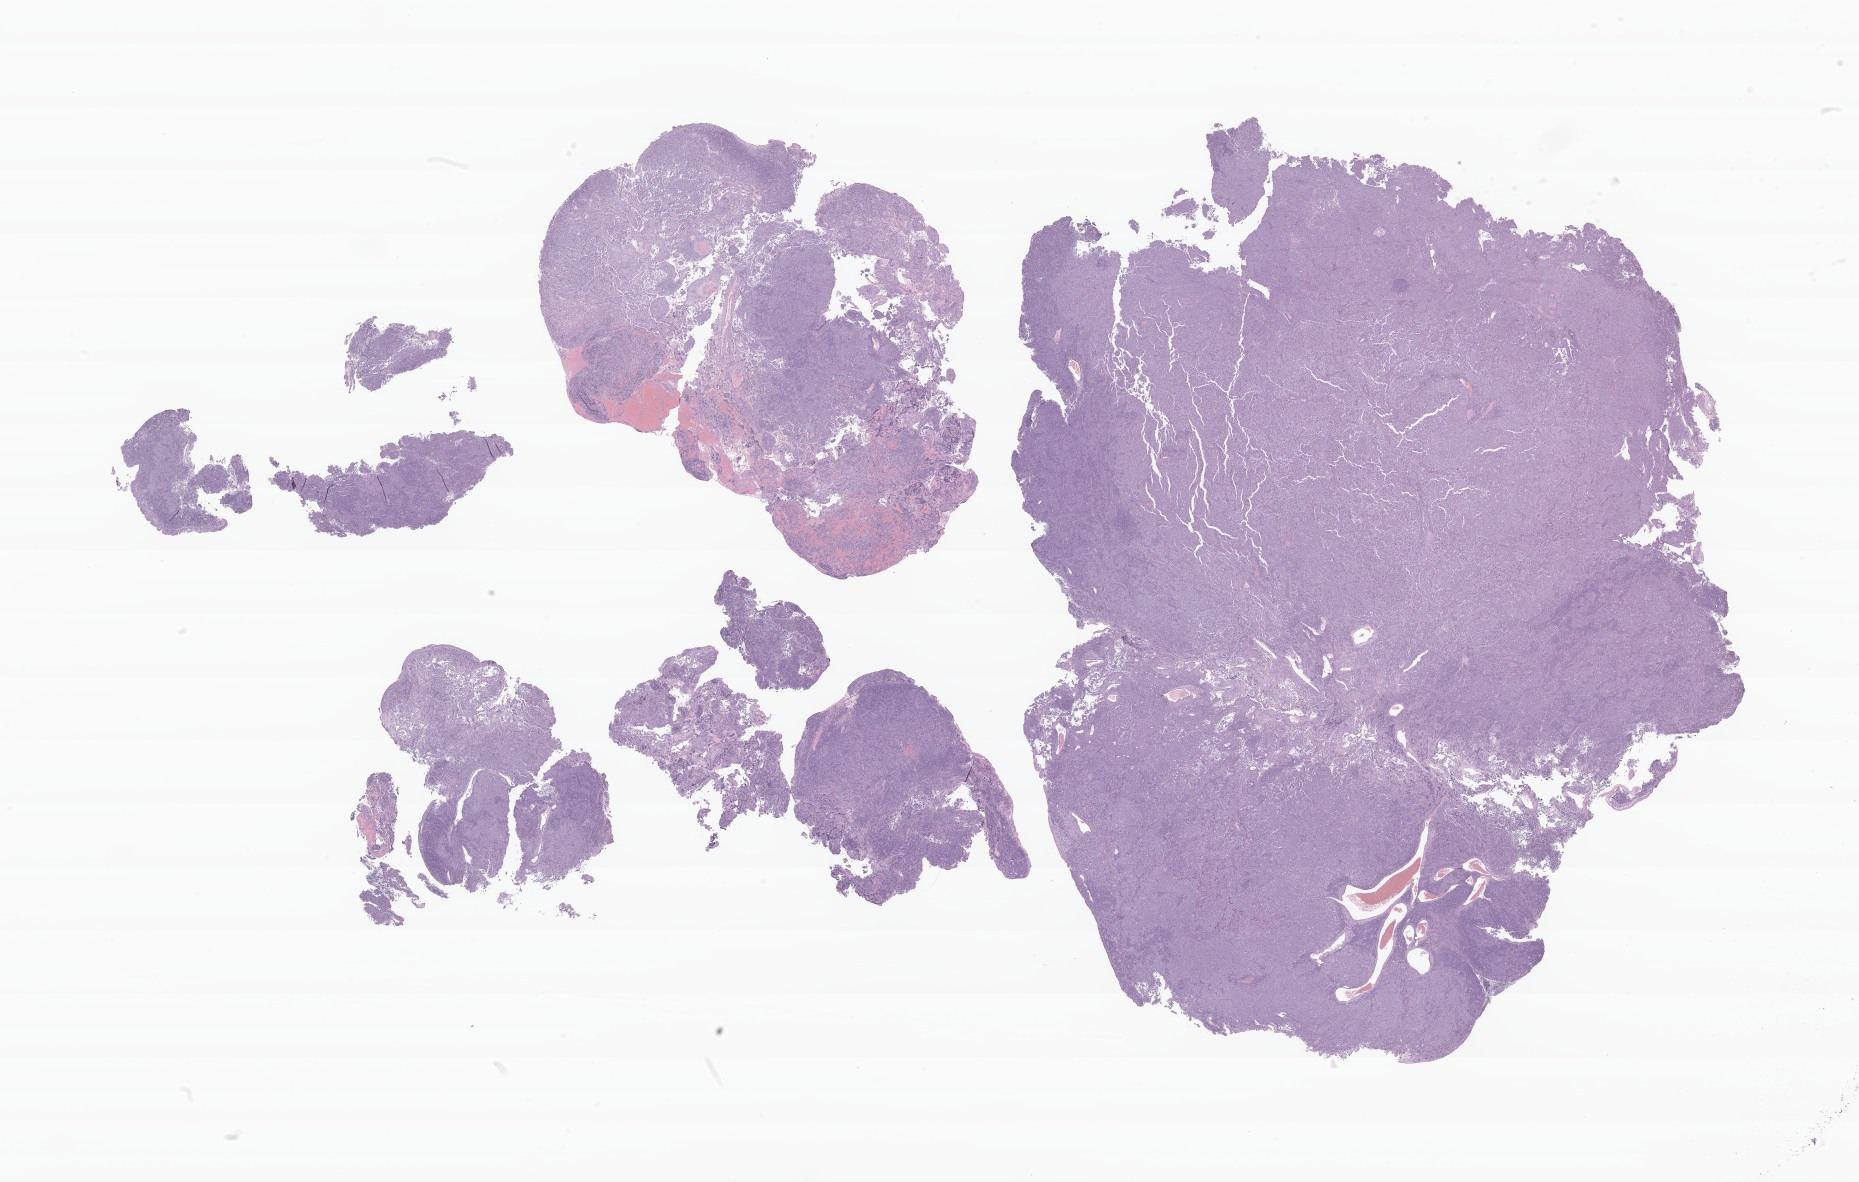
Whole-slide image, hematoxylin and eosin (H&E) stain of tumor tissue from the nasal cavity, low-resolution overview of the scanned area, about 31.3 x 19.9 mm; formalin-fixed, paraffin-embedded (FFPE) tissue. Patient: male, age 180 months (15 years).
Diagnosis (ICD-O-3 morphology term): Carcinoma, NOS.